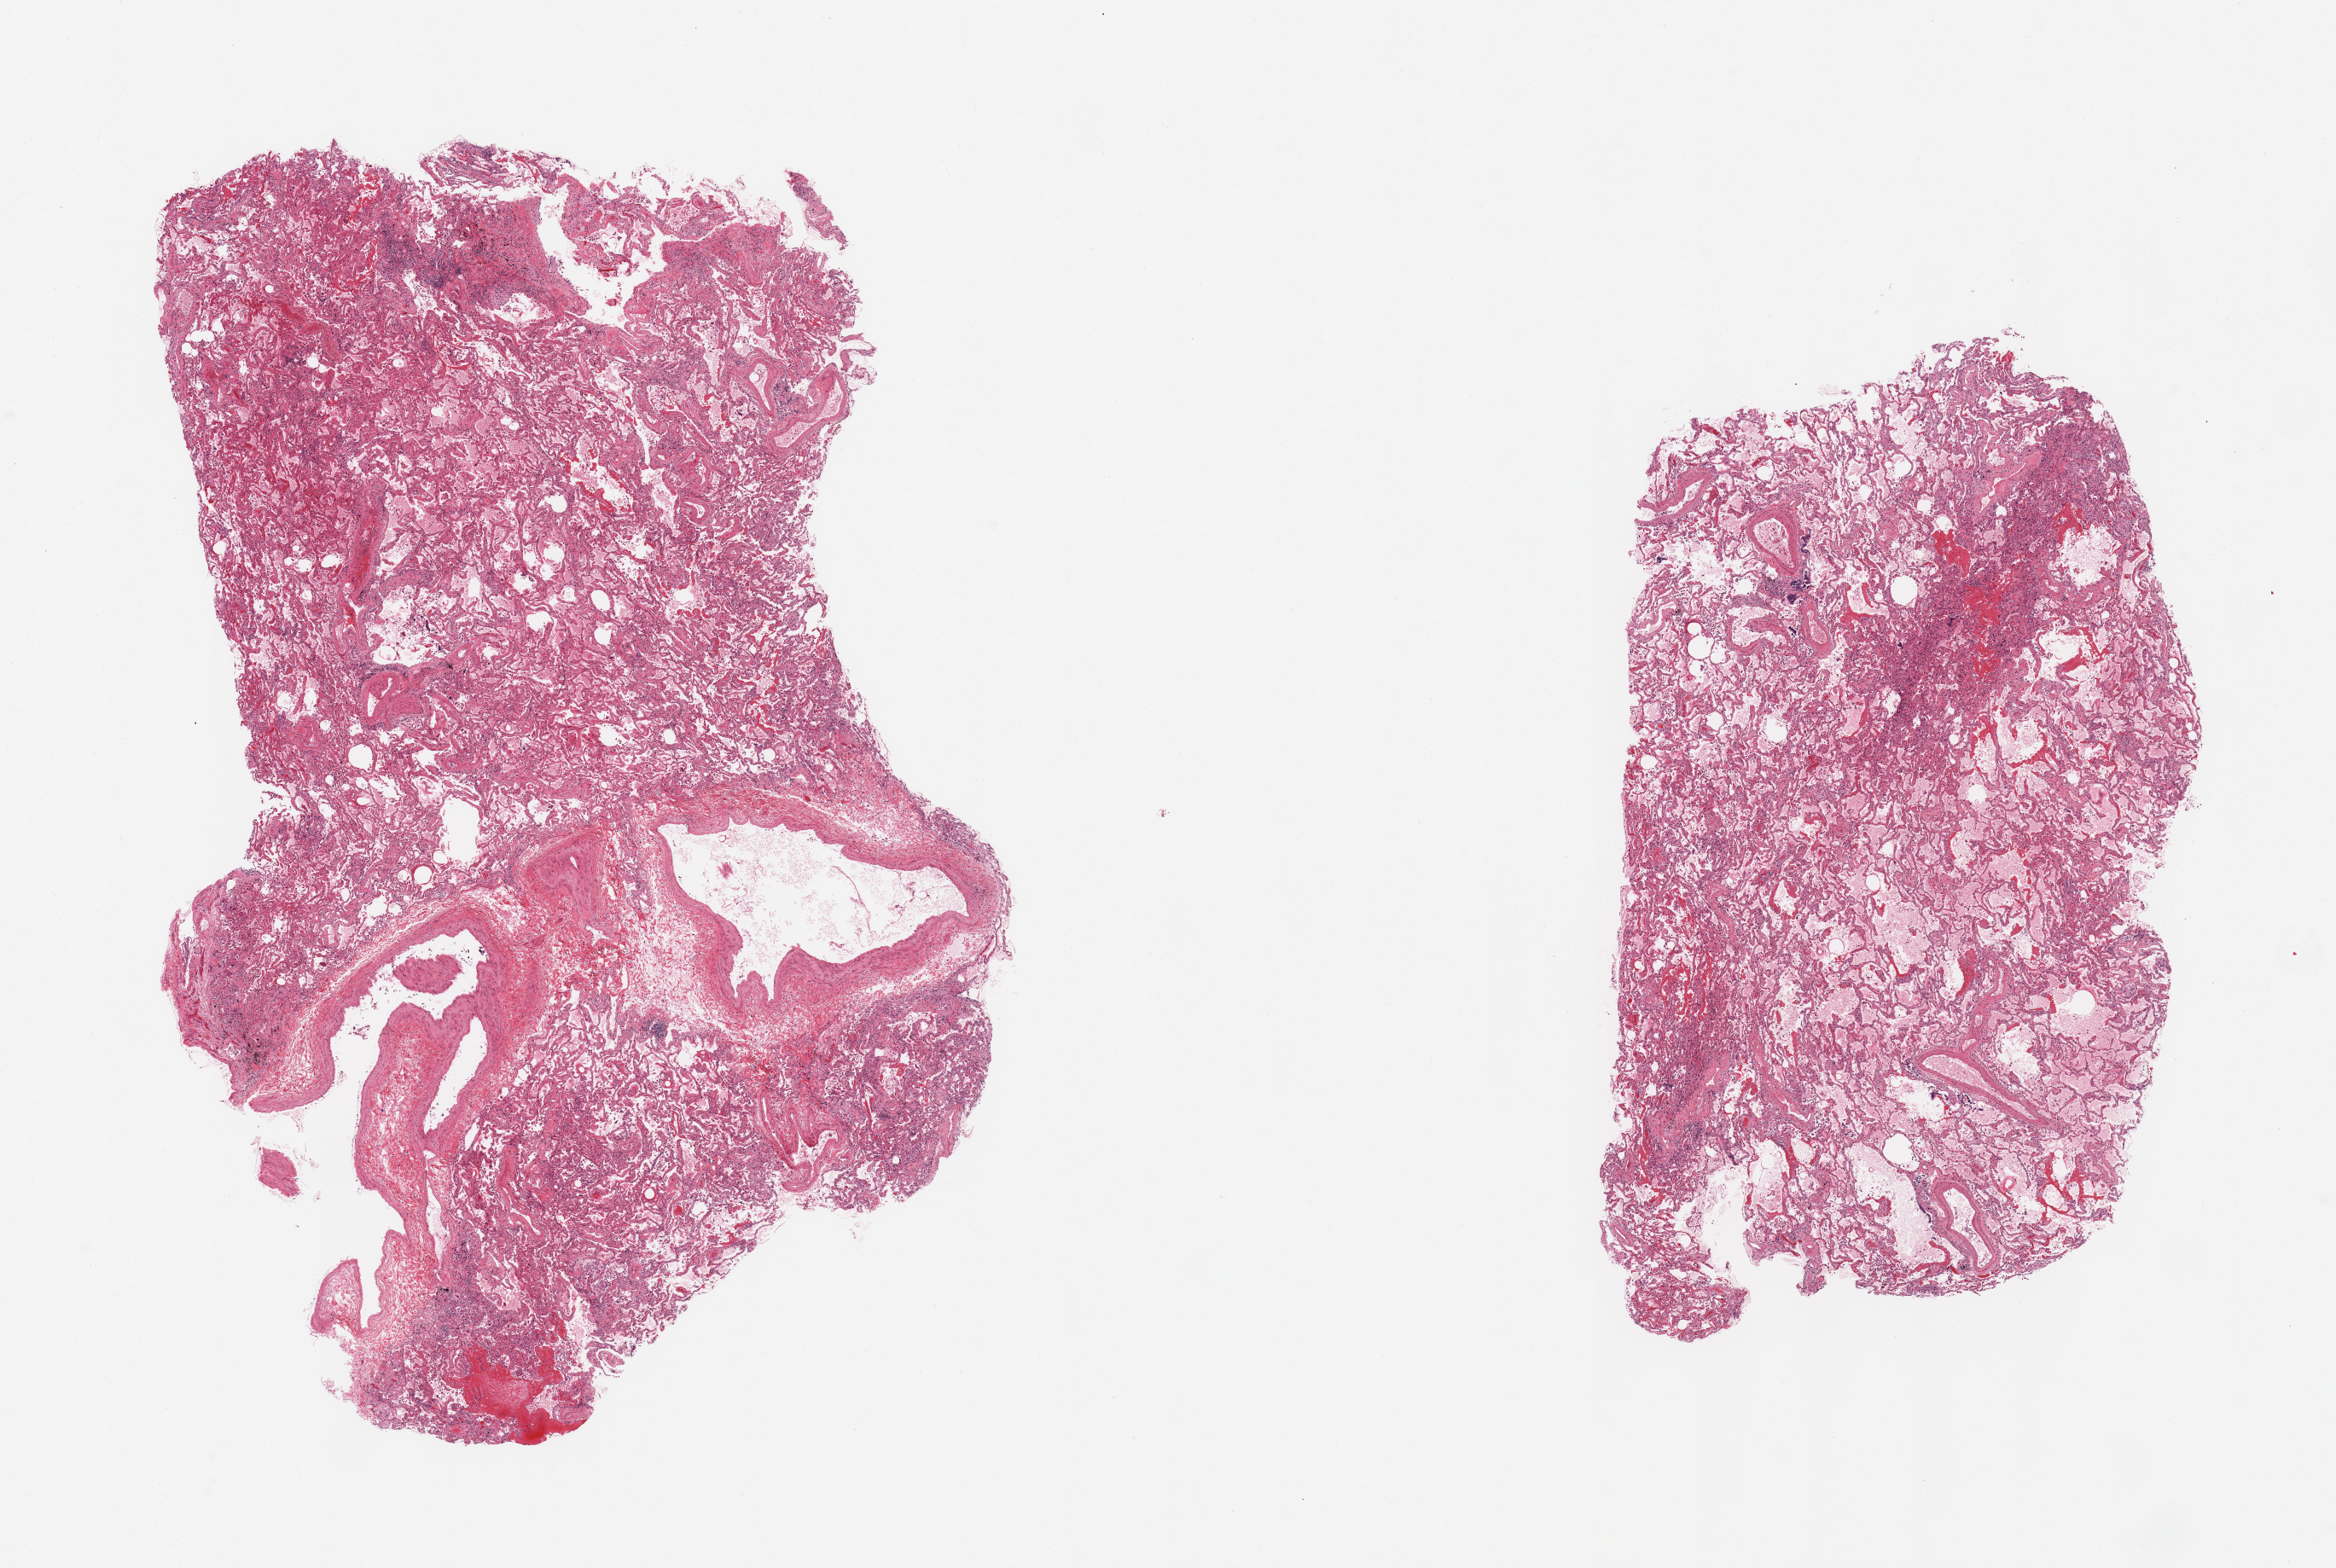
Digitized hematoxylin and eosin (H&E)-stained section, whole scanned area (about 21.7 x 14.5 mm, acquisition: 20x scan) shown as a low-resolution overview. PAXgene-fixed, paraffin-embedded tissue. Sampled site (target tissue): lung. Tissue donor sample. Donor: male.
- pathologist's review note for this sample: 2 pieces patchy chronic fibrosing pneumonitis; fibrin aggregates noted